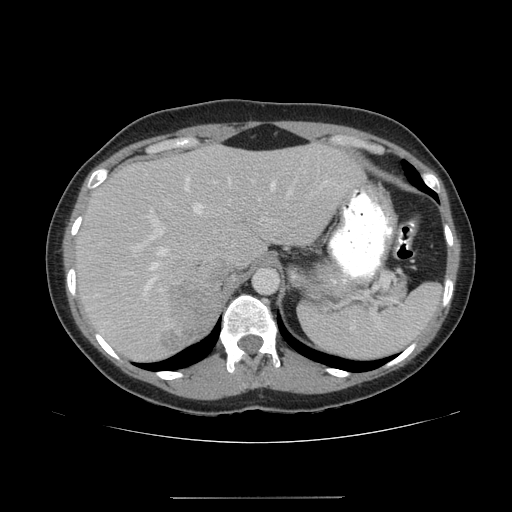
Contrast-enhanced abdominal CT, one axial slice; slice 125 of 161 in the series (ordered by position); reconstruction kernel STANDARD; soft-tissue window (W 400 / L 40 HU); 512 × 512 image matrix. Female patient. Case-level facts recorded for this patient, not image findings: diagnosis: adrenocortical carcinoma; tumour side: right adrenal; tumour size at pathology: 9 cm; Ki-67 index: 14 %; stage (as recorded): 3.
Structures marked on this image (semi-automatic segmentation, software-assisted and operator-edited):
- mass: bounding box [x1, y1, x2, y2] px = [162, 260, 234, 349]